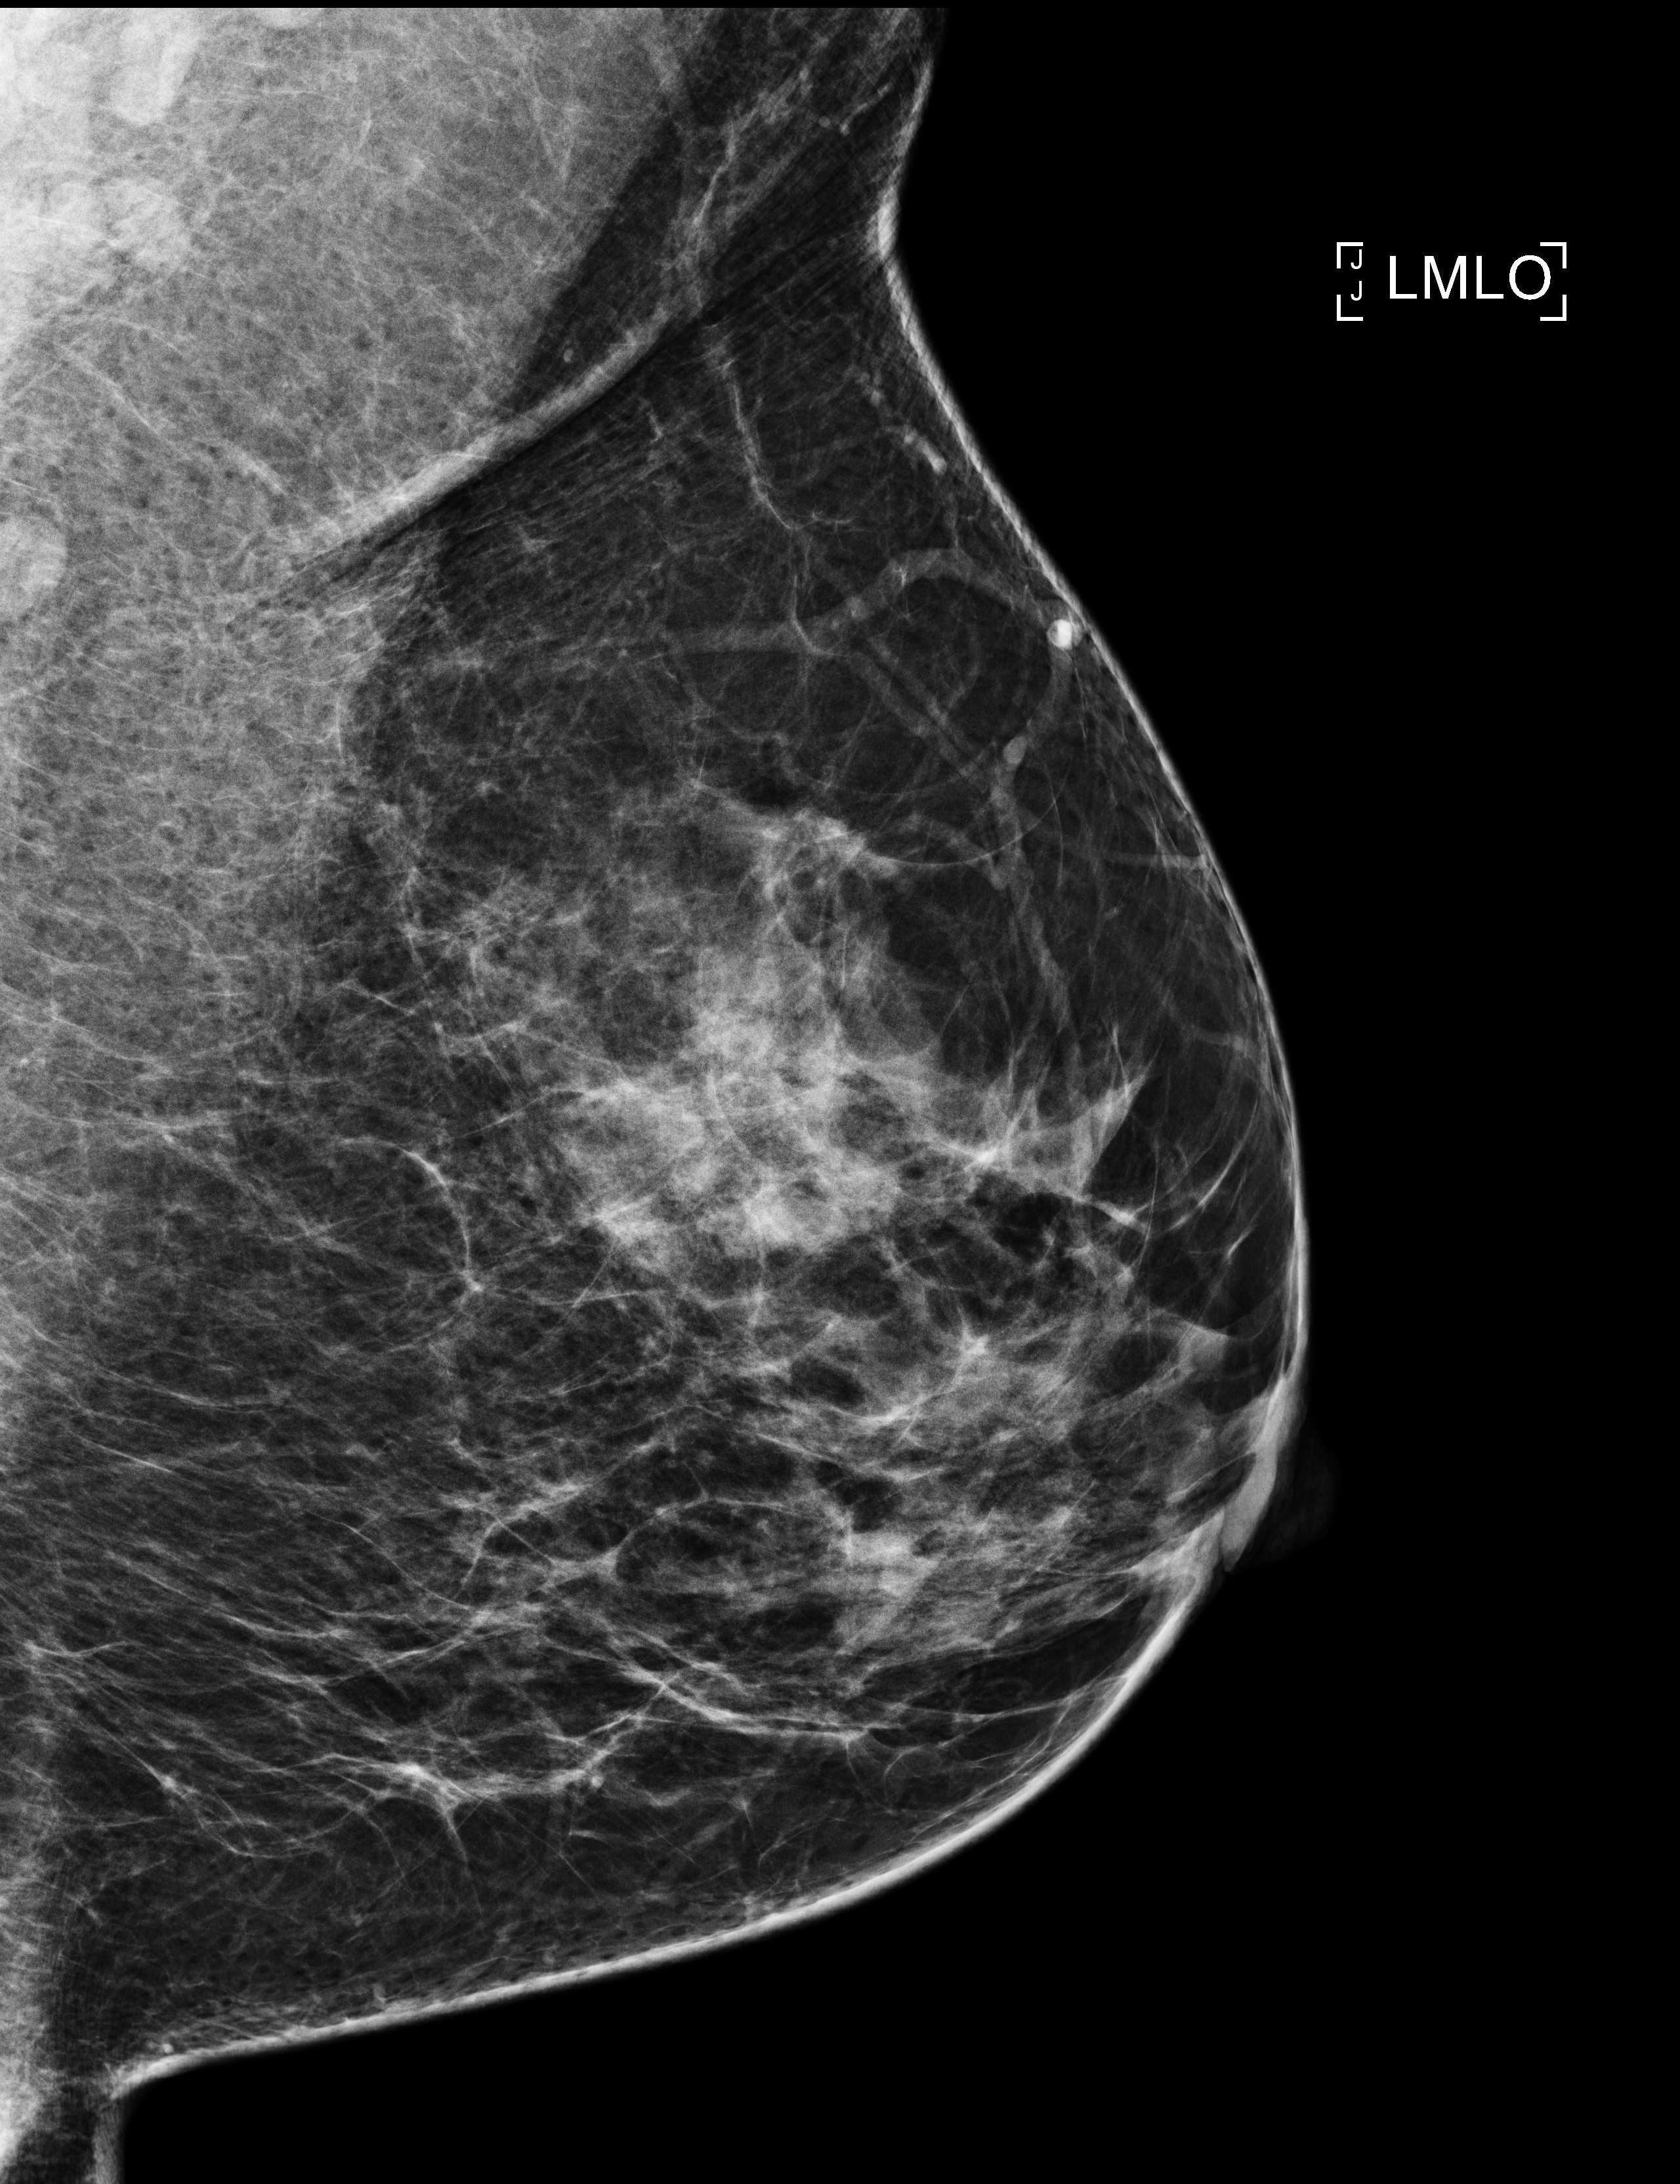
Digital mammogram (FFDM), left breast, medio-lateral oblique projection, annual screening mammography examination, system: Selenia Dimensions. Patient aged 53 years (female).
- BI-RADS breast density category at the screening exam (both breasts, scale 1–4): 2
- final BI-RADS assessment for this screening round (tomosynthesis exam, both breasts): category 1
- recall: no recall after this screen